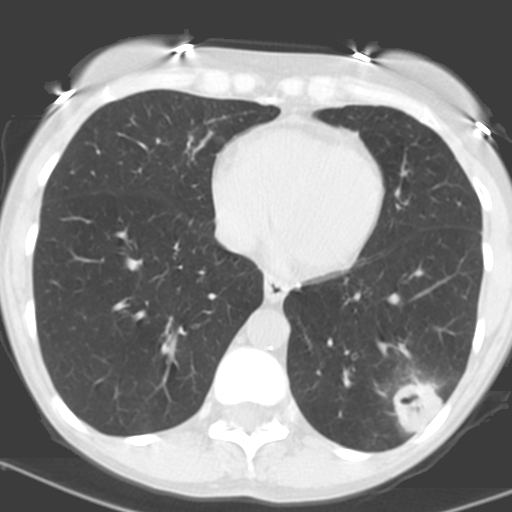
Low-dose screening chest CT, one axial slice. Position 56 of 156 along the scan axis. Lung window (W 1500 / L -600 HU). 512 × 512 image matrix, field of view 262 × 262 mm.
Structures marked on this image (manually delineated by an expert):
- lesion 1 (tumor, lower lobe of left lung): bounding box [x1, y1, x2, y2] px = [391, 376, 441, 435]